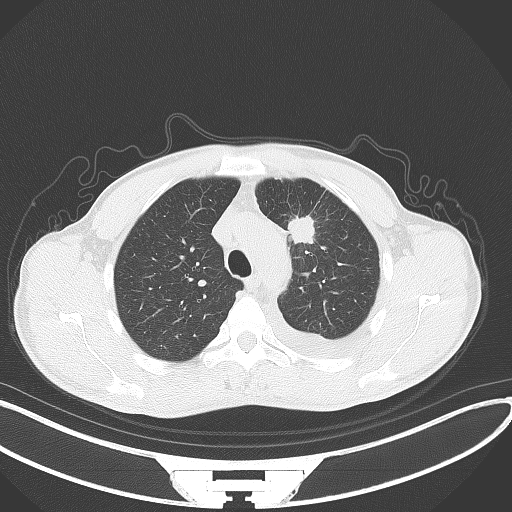
Chest CT, one axial slice. Position 100 of 130 along the scan axis. Reconstruction kernel B70f. 120 kVp. Lung window (W 1500 / L -600 HU). 512 × 512 image matrix. Male patient, age 49 years. Case-level facts recorded for this patient, not image findings: clinical TNM (as recorded): T1c N1 M1.
Structures marked on this image (rectangle marked by the reading radiologist):
- lung tumour (recorded histology: adenocarcinoma): bounding box (x1, y1, x2, y2) in pixels: (287, 216, 326, 250)